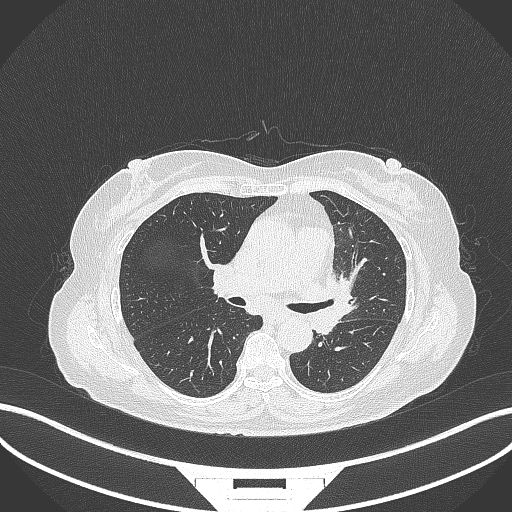
Chest CT, one axial slice. Slice 191 of 382 in the series (ordered by position). 120 kVp. Lung window (W 1500 / L -600 HU). 512 × 512 image matrix. Female patient, age 64 years. From the clinical record (not read from this slice): clinical TNM (as recorded): T2a N2 M0.
Structures marked on this image (rectangle marked by the reading radiologist):
- lung tumour (recorded histology: adenocarcinoma): bounding box <311,268,355,339> (left, top, right, bottom; pixels)